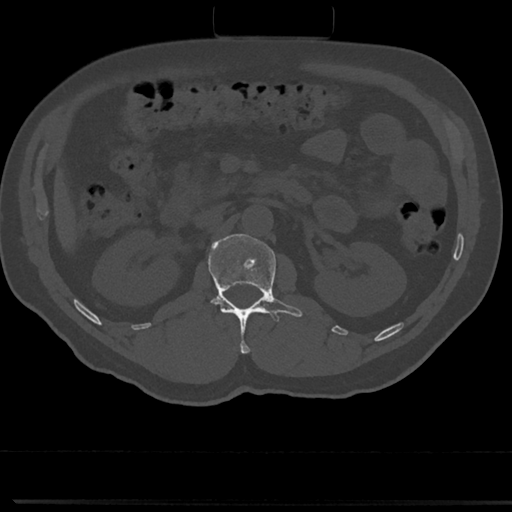
CT including the spine, one axial slice. Slice 75 of 817 in the series (ordered by position). 120 kVp. Bone window (W 1800 / L 400 HU). 512 × 512 image matrix, field of view 355 × 355 mm. Patient: male, 61 years. From the clinical record (not read from this slice): primary cancer: prostate.
Annotated regions visible in this slice (semi-automatic segmentation, software-assisted and operator-edited):
- L1 vertebra: bounding box [x1, y1, x2, y2] px = [191, 235, 301, 352]